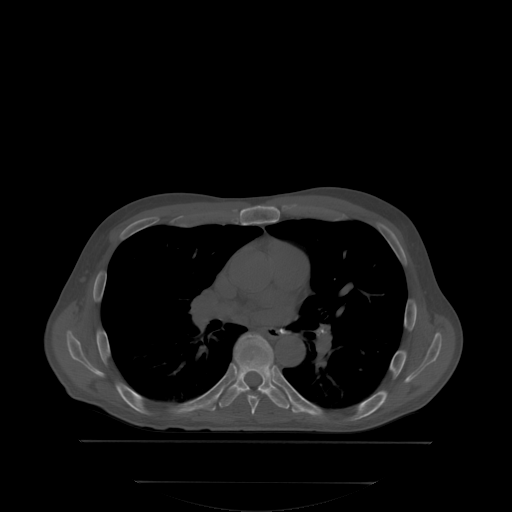
CT including the spine, one axial slice; position 231 of 350 along the scan axis; bone window (W 1800 / L 400 HU); 2.5 mm slice thickness; 512 × 512 image matrix, field of view 500 × 500 mm. Male patient, age 58 years. From the clinical record (not read from this slice): primary cancer: prostate; vertebrae with lytic lesions (as recorded): L1.
Annotated regions visible in this slice (semi-automatically segmented with operator editing):
- T6 vertebra: bounding box <243,384,290,414> (left, top, right, bottom; pixels)
- T7 vertebra: <219,334,289,408>